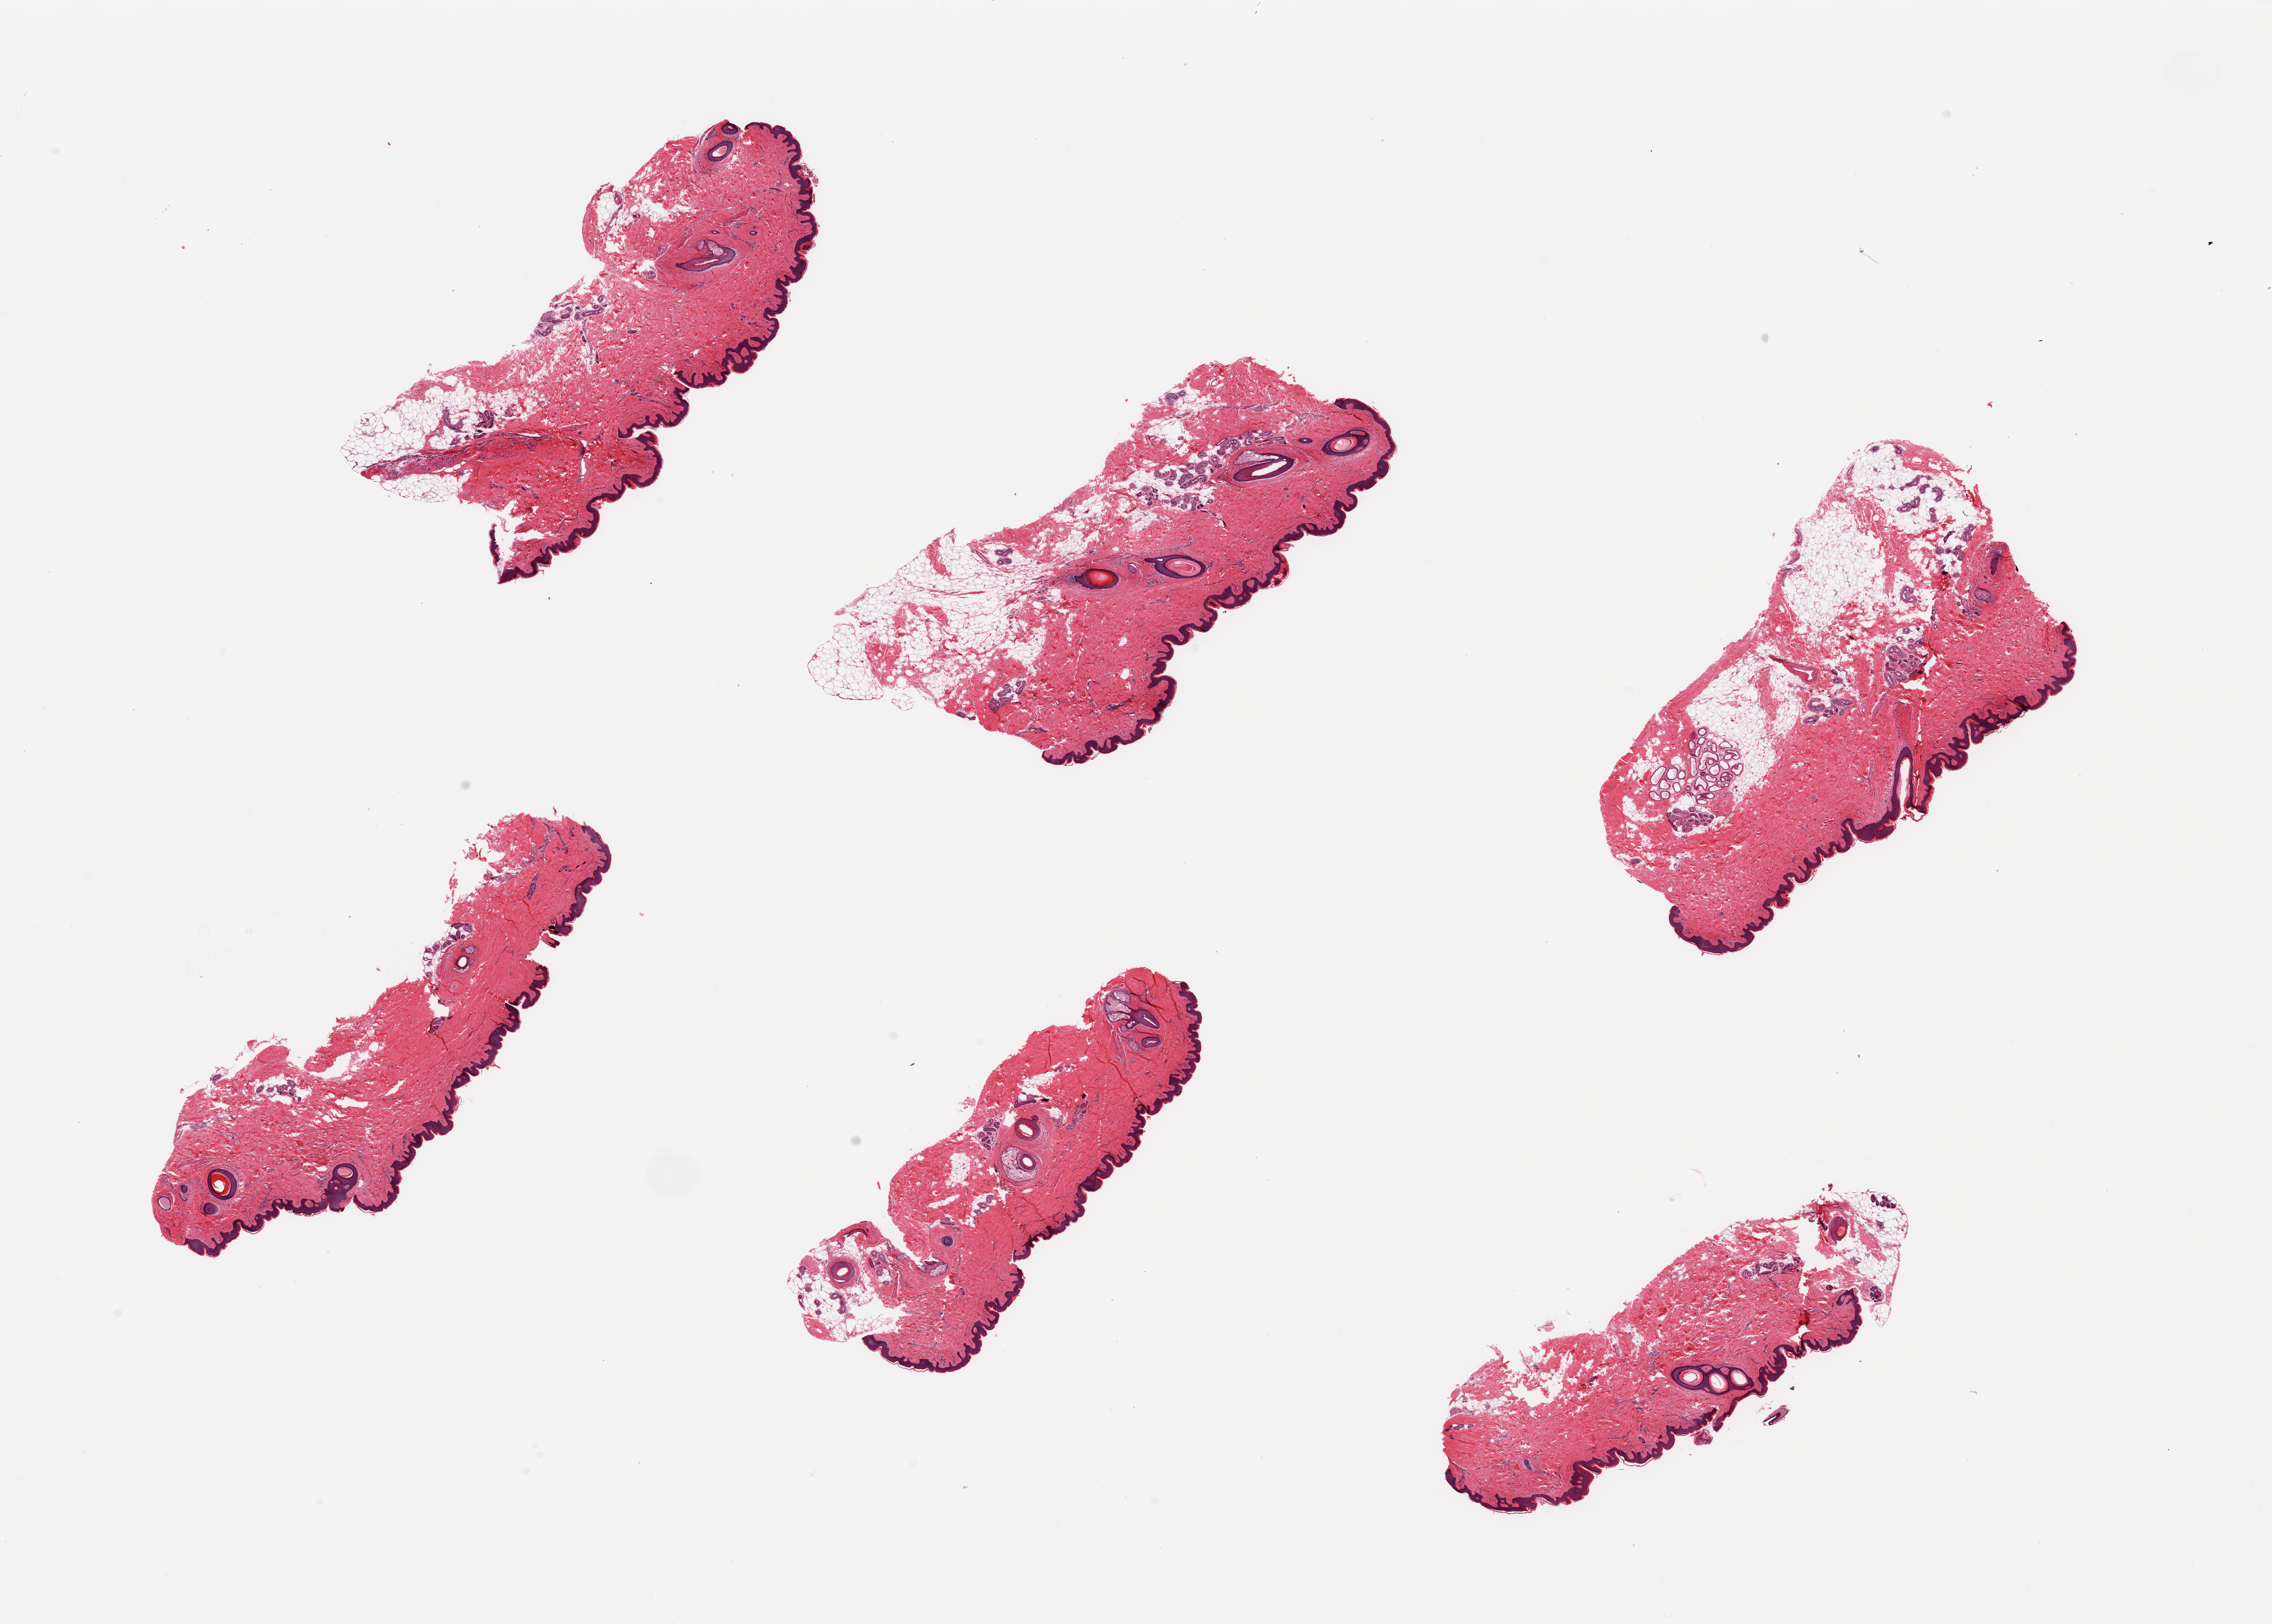
Digitized hematoxylin and eosin (H&E)-stained section — low-resolution overview of the scanned area, about 26.6 x 19.0 mm (acquisition: 20x scan), PAXgene-fixed paraffin-embedded (PFPE) section, sampled site (target tissue): skin of suprapubic region, tissue donor sample. Donor: male.
Reviewer comment on this tissue sample: 6 pieces; one piece well trimmed, other pieces contain from 5% to 40% subcutaneous fat.